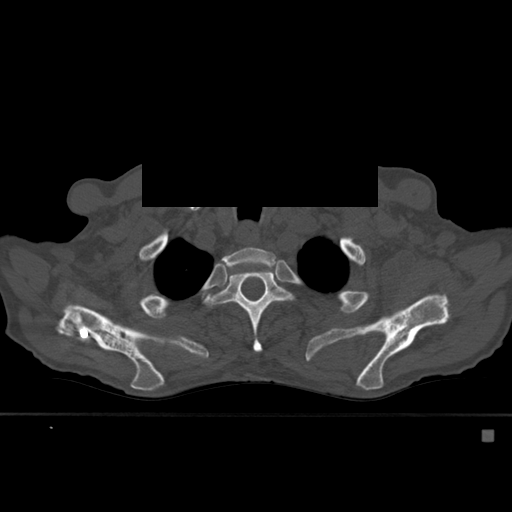
CT including the spine, one axial slice. Slice 435 of 527 in the series (ordered by position). Bone window (W 1800 / L 400 HU). 512 × 512 image matrix, field of view 373 × 373 mm. Male patient, age 78 years. From the clinical record (not read from this slice): primary cancer: prostate.
Annotated regions visible in this slice (semi-automatically segmented with operator editing):
- T2 vertebra: bounding box (x1, y1, x2, y2) in pixels: (222, 247, 276, 278)
- T3 vertebra: (207, 268, 292, 353)